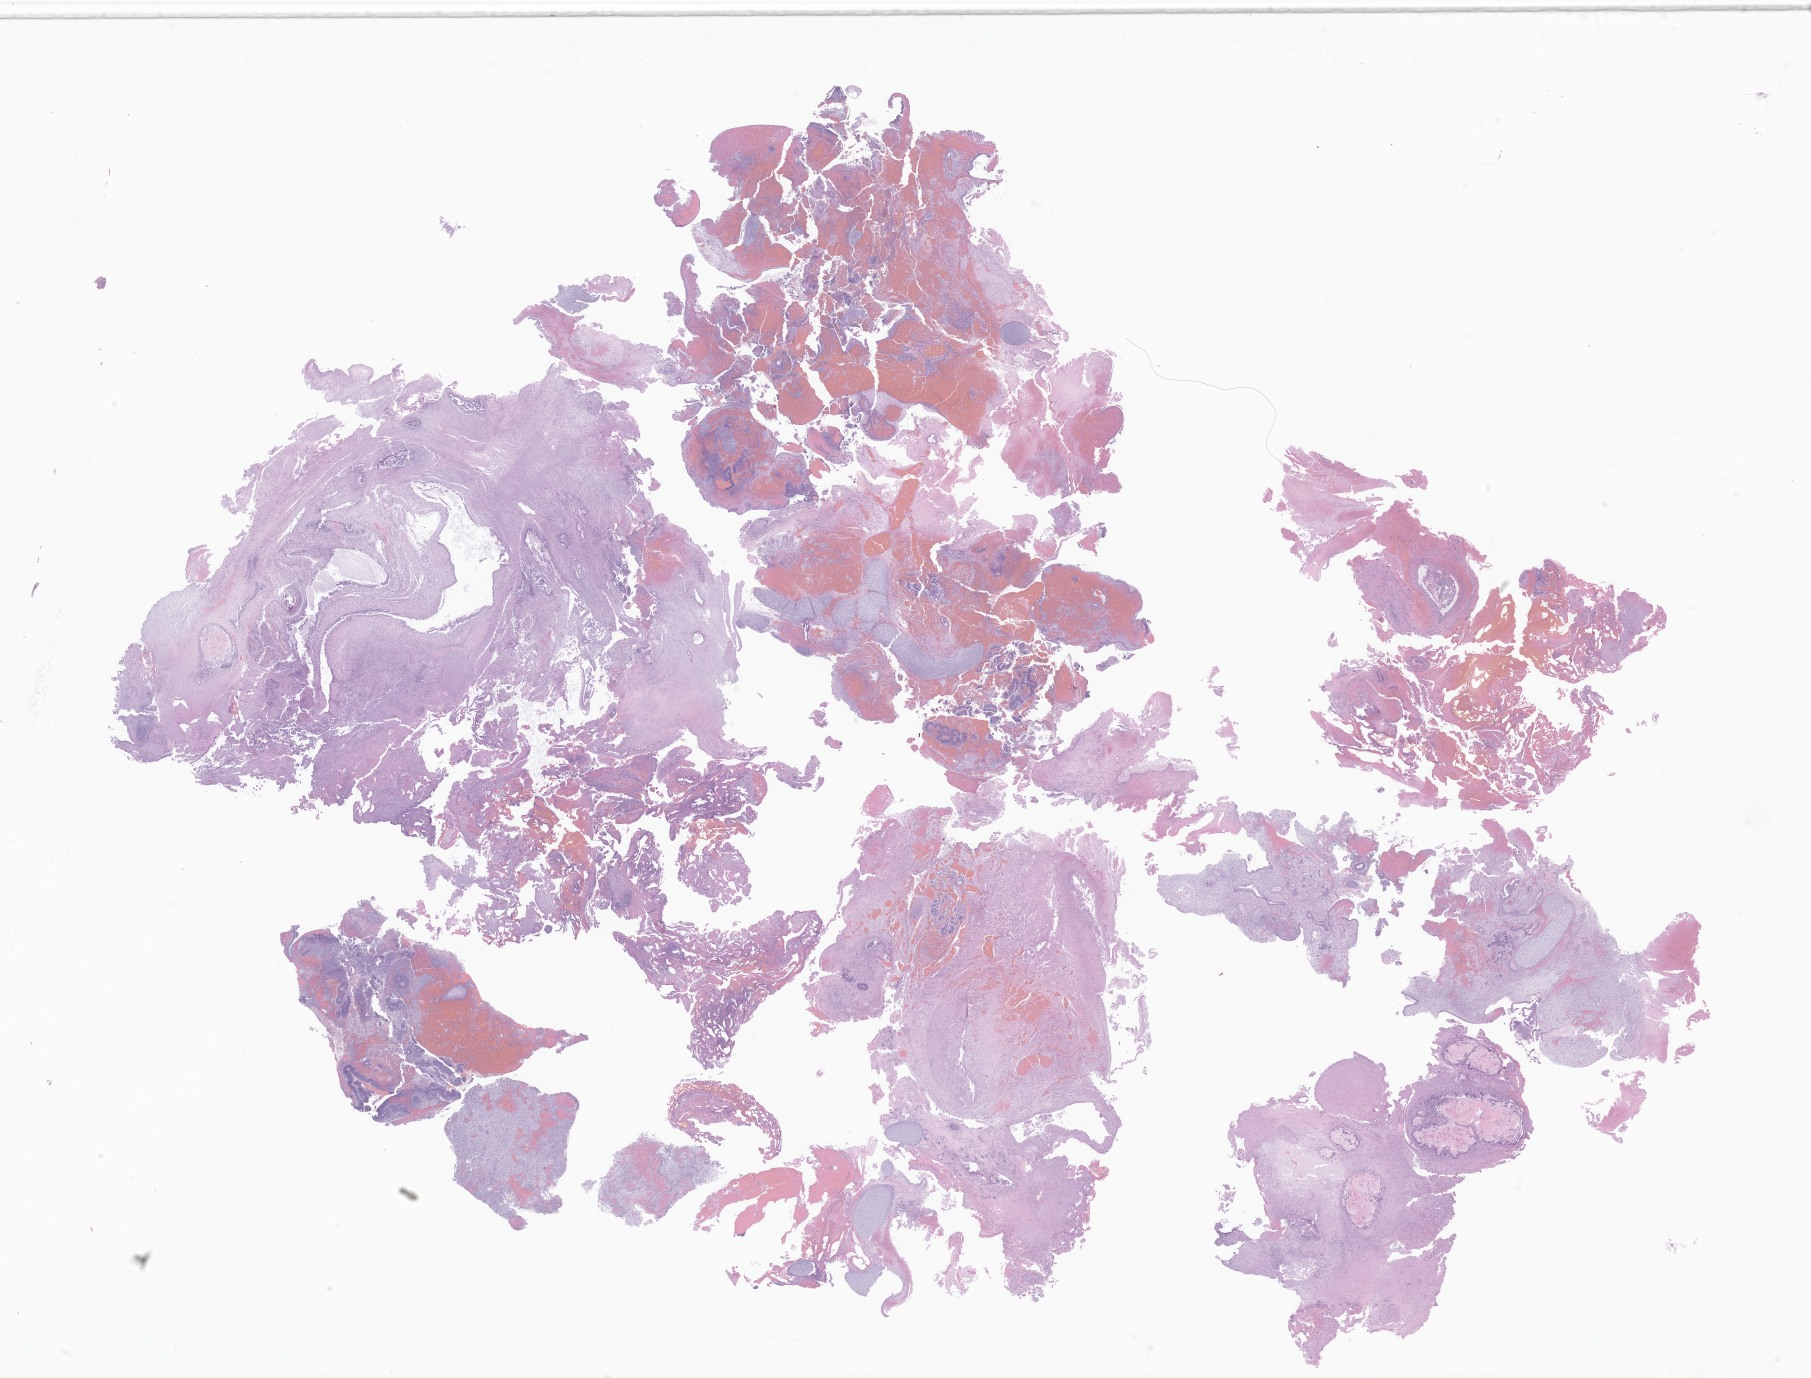
Digitized haematoxylin and eosin-stained section of tumor tissue from the brain — whole scanned area (about 30.5 x 23.2 mm) shown as a low-resolution overview. FFPE section. Male patient, age 49 months (4 years 1 month).
Diagnosis (ICD-O-3 morphology term): Mixed germ cell tumor.